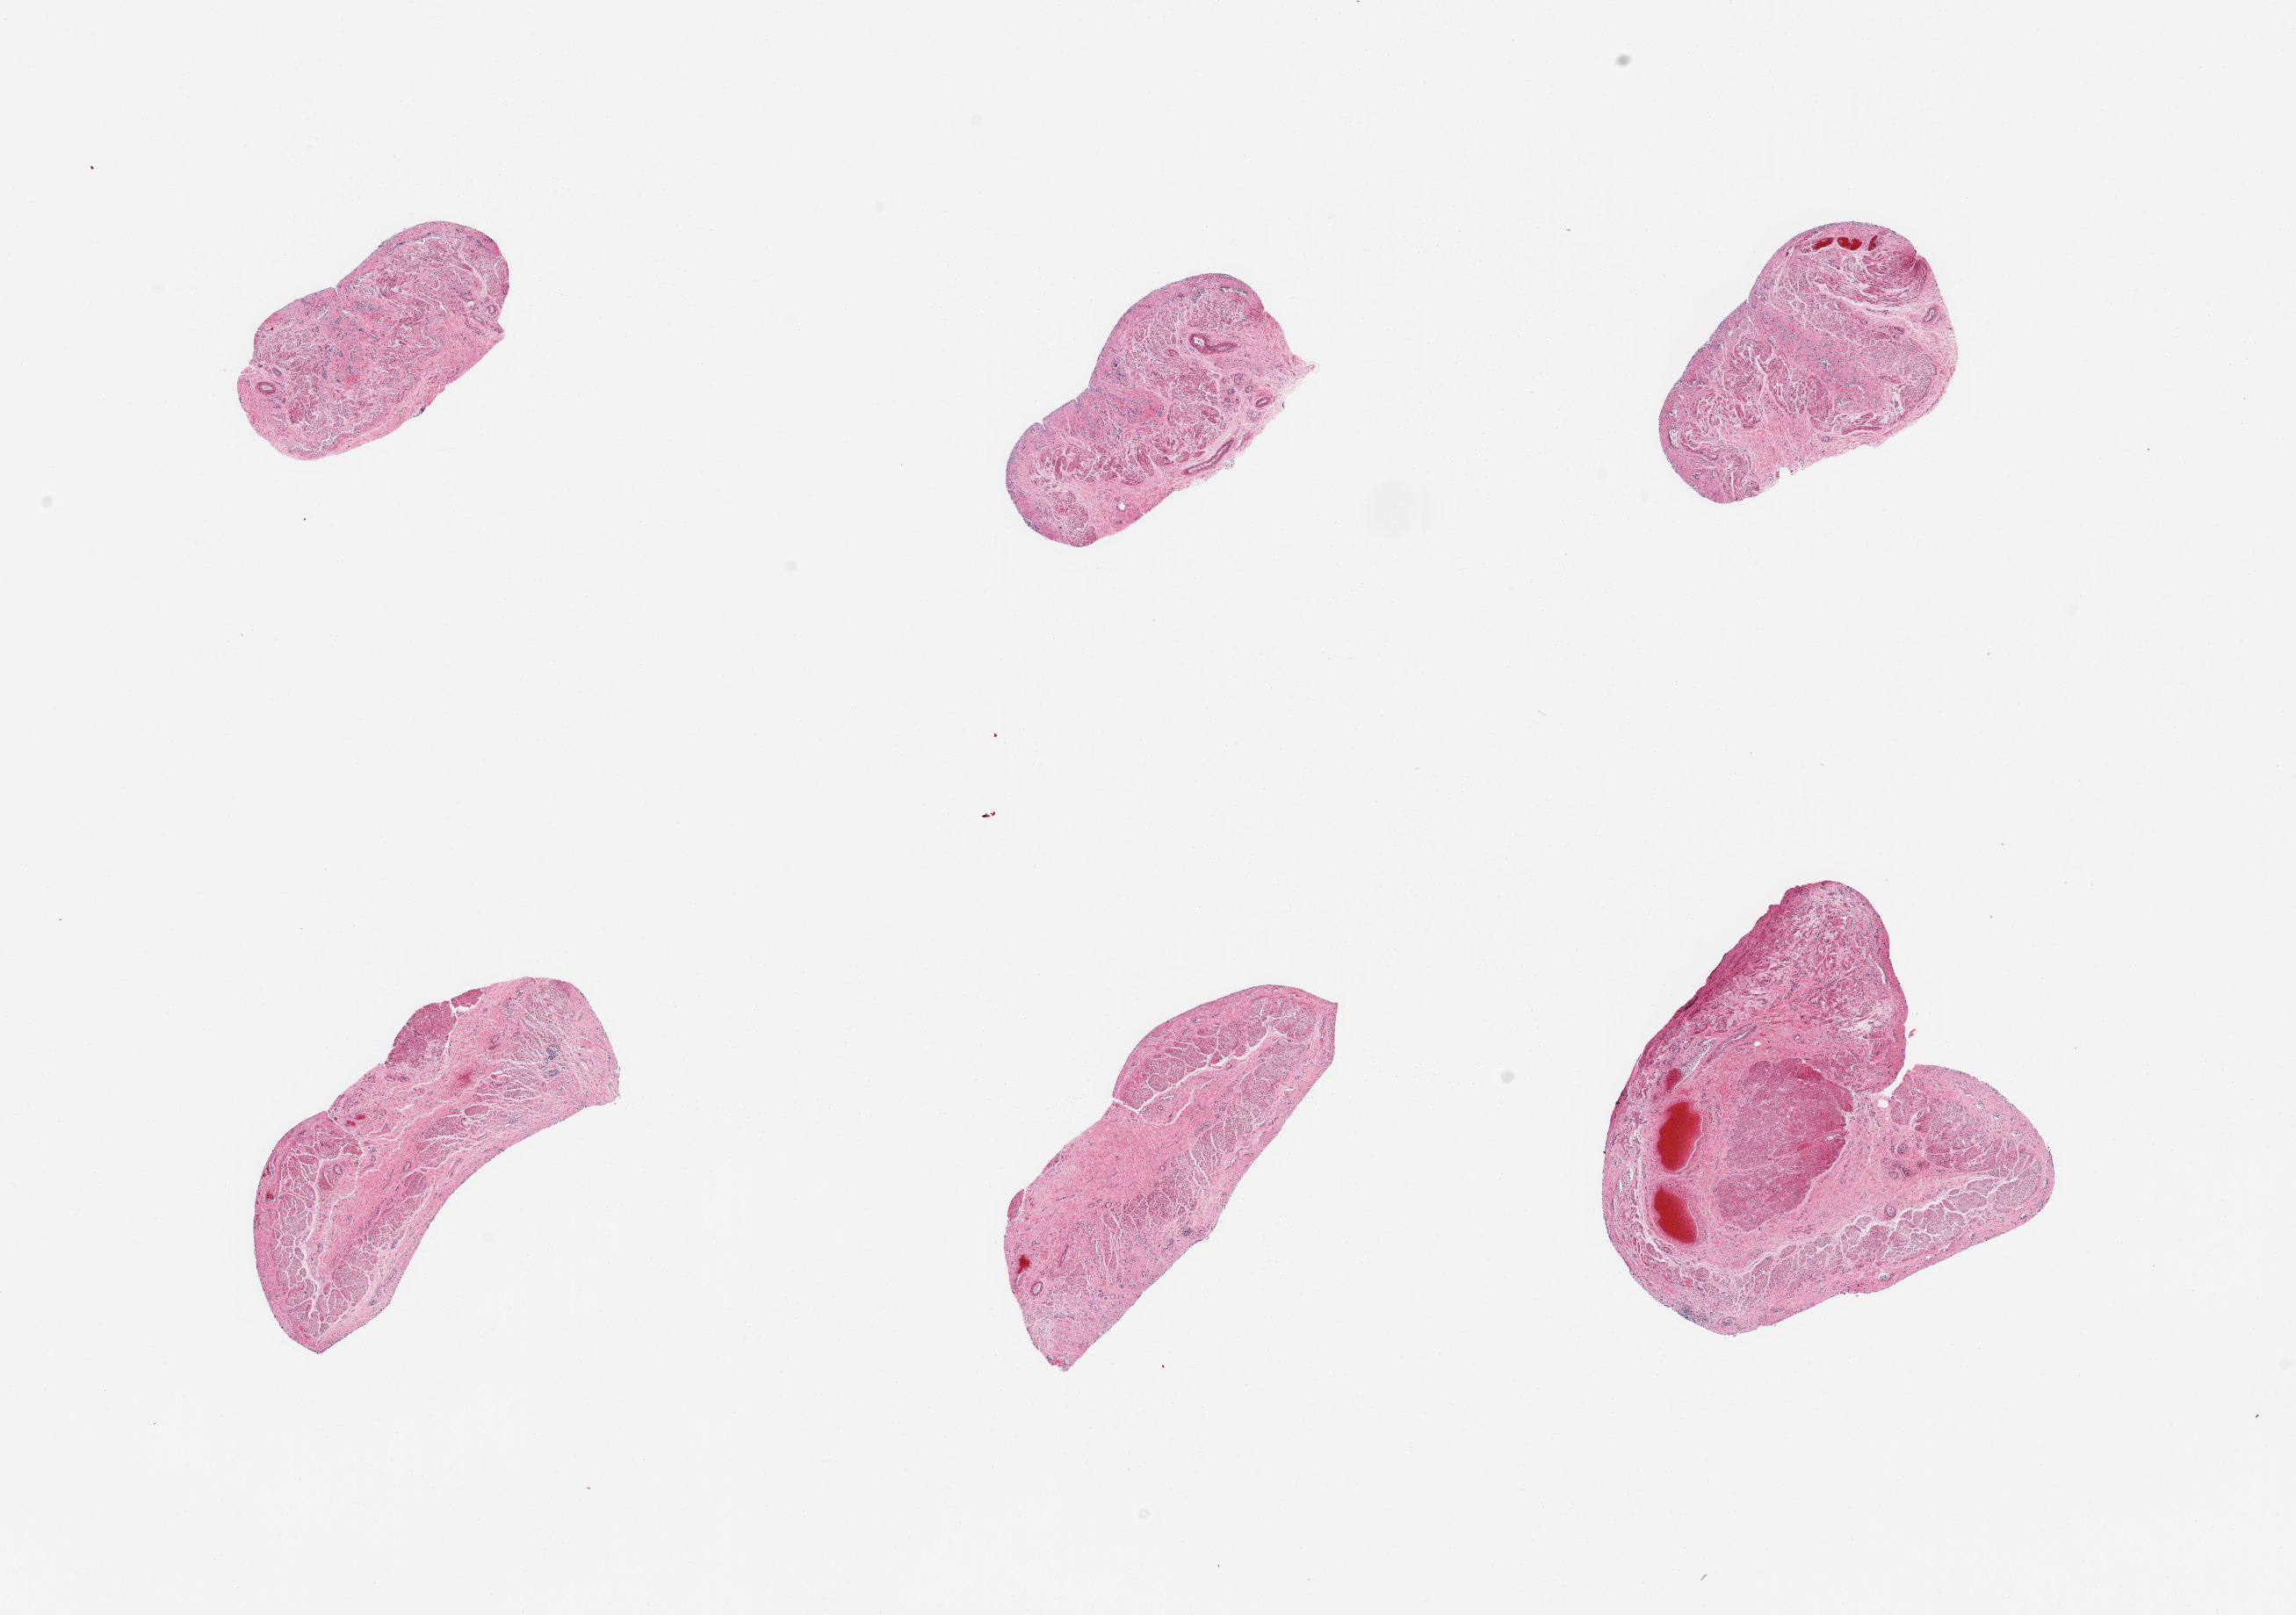
Hematoxylin and eosin (H&E) whole-slide image, low-resolution overview of the scanned area, about 20.7 x 14.5 mm (acquisition: 20x scan). PAXgene-fixed paraffin-embedded (PFPE) section. Target tissue: esophageal mucous membrane. Tissue donor sample. Donor: male.
- review note (as recorded): 6 pieces; target mucosa not present; well preserved muscularis